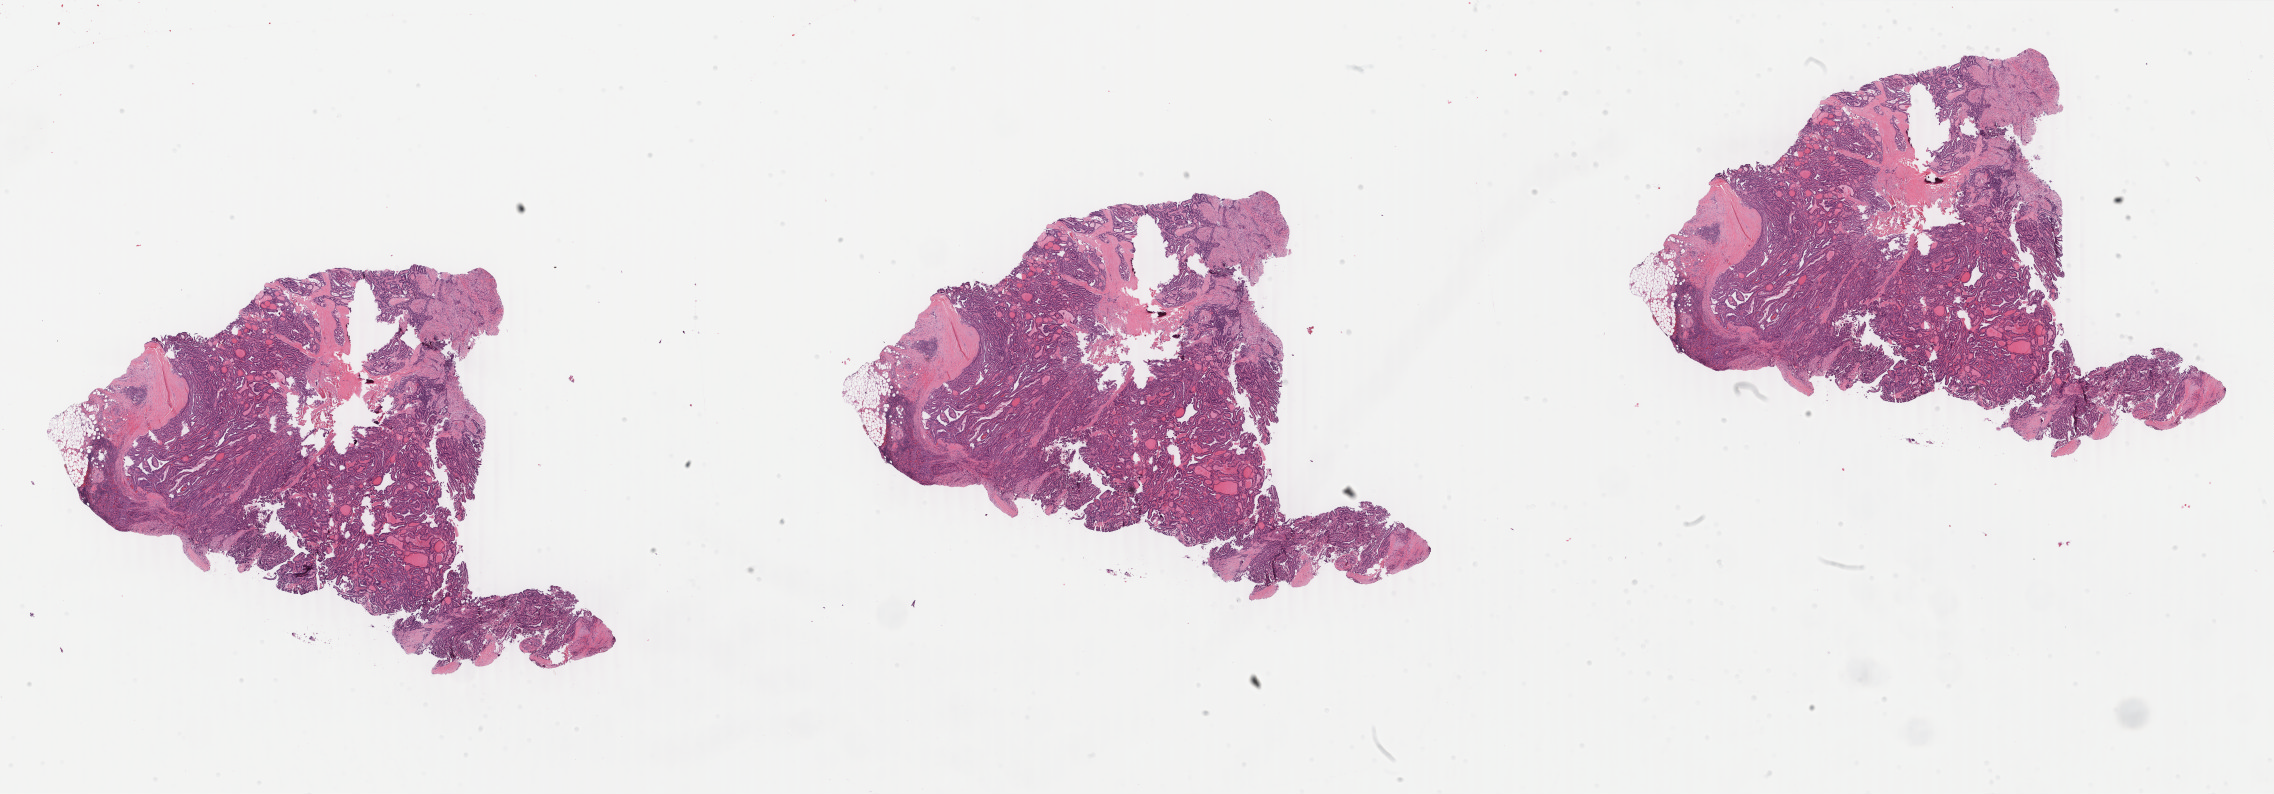
Digitized H&E tissue section (whole slide) — shown as a low-resolution overview of the whole scanned area (about 36.2 x 12.6 mm). Formalin-fixed paraffin-embedded (FFPE) diagnostic section. Primary tumour sample from the thyroid. Female, age 33 years at initial diagnosis.
* diagnosis: Papillary adenocarcinoma, NOS (thyroid gland)
* laterality: right
* AJCC pathologic stage: I (7th edition)
* TNM: T2 N1b MX